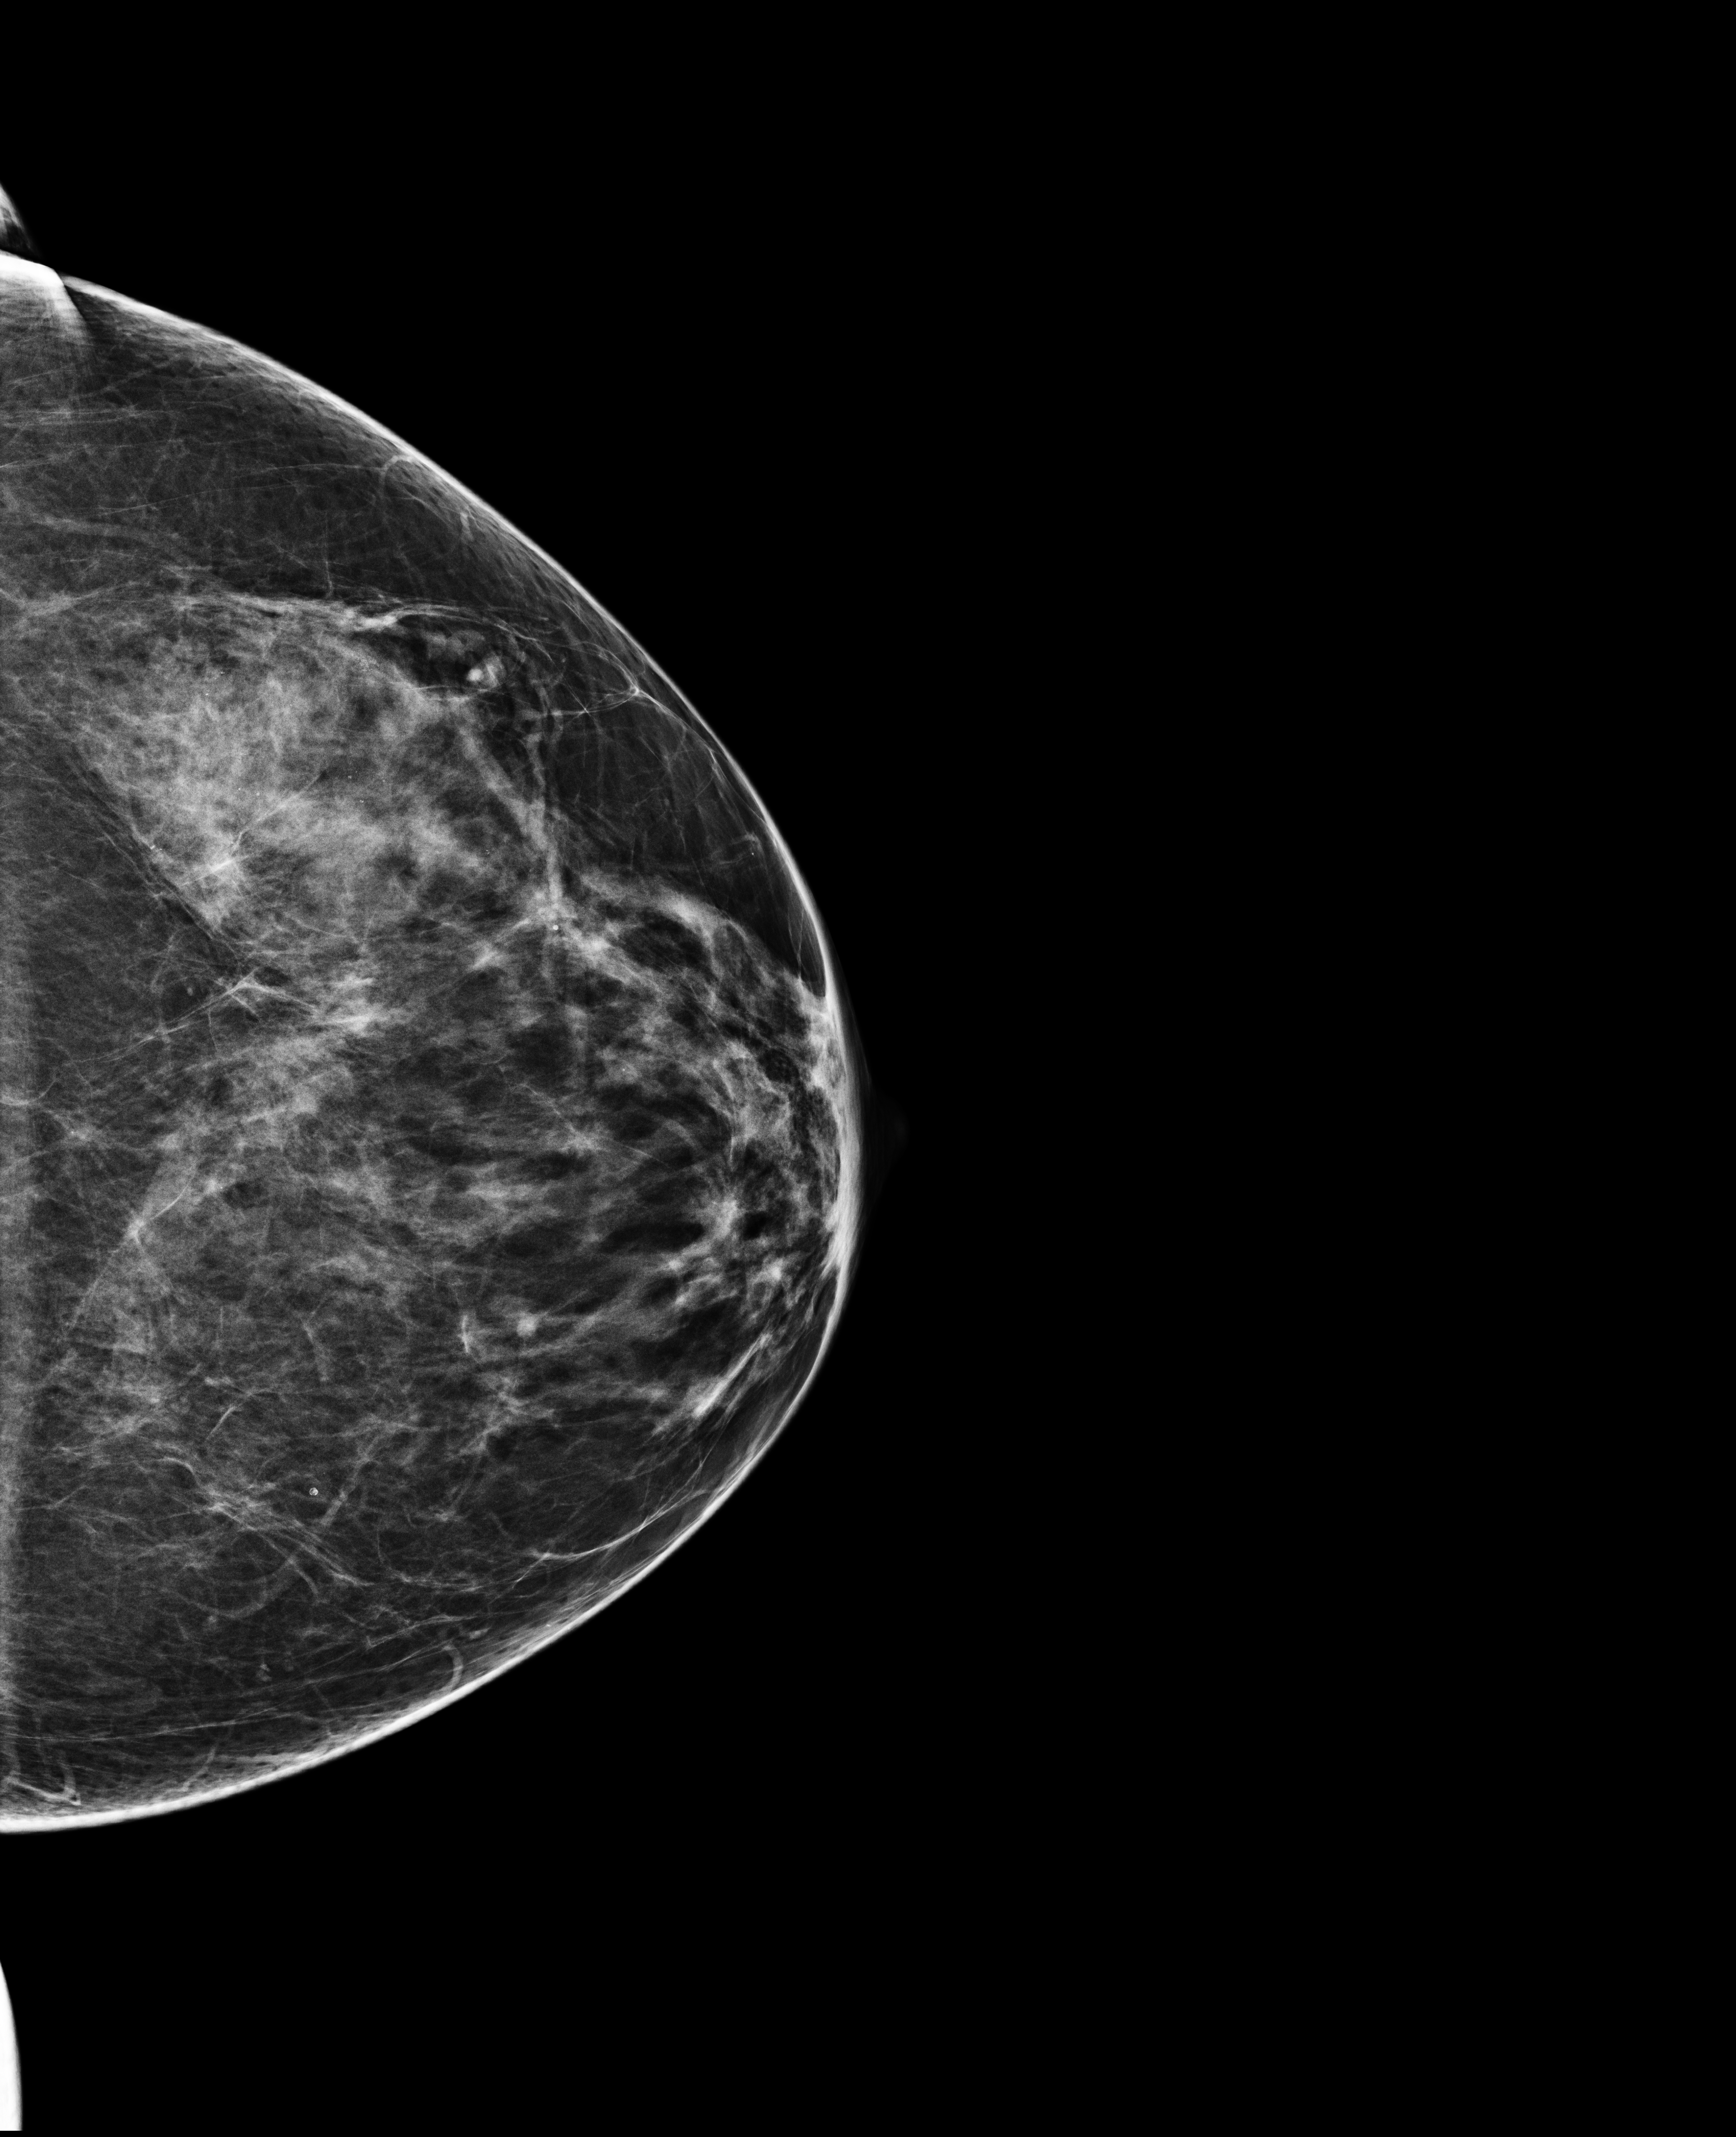
Full-field digital mammogram (FFDM), left breast, cranio-caudal projection, screening examination, compressed breast thickness 64 mm, system: Selenia Dimensions. Patient: female, 59 years.
BI-RADS breast density category at the screening exam (both breasts, scale 1–4): 3. Final BI-RADS category for the screening round (tomosynthesis exam, both breasts): category 2. Recall: no recall after this screen.